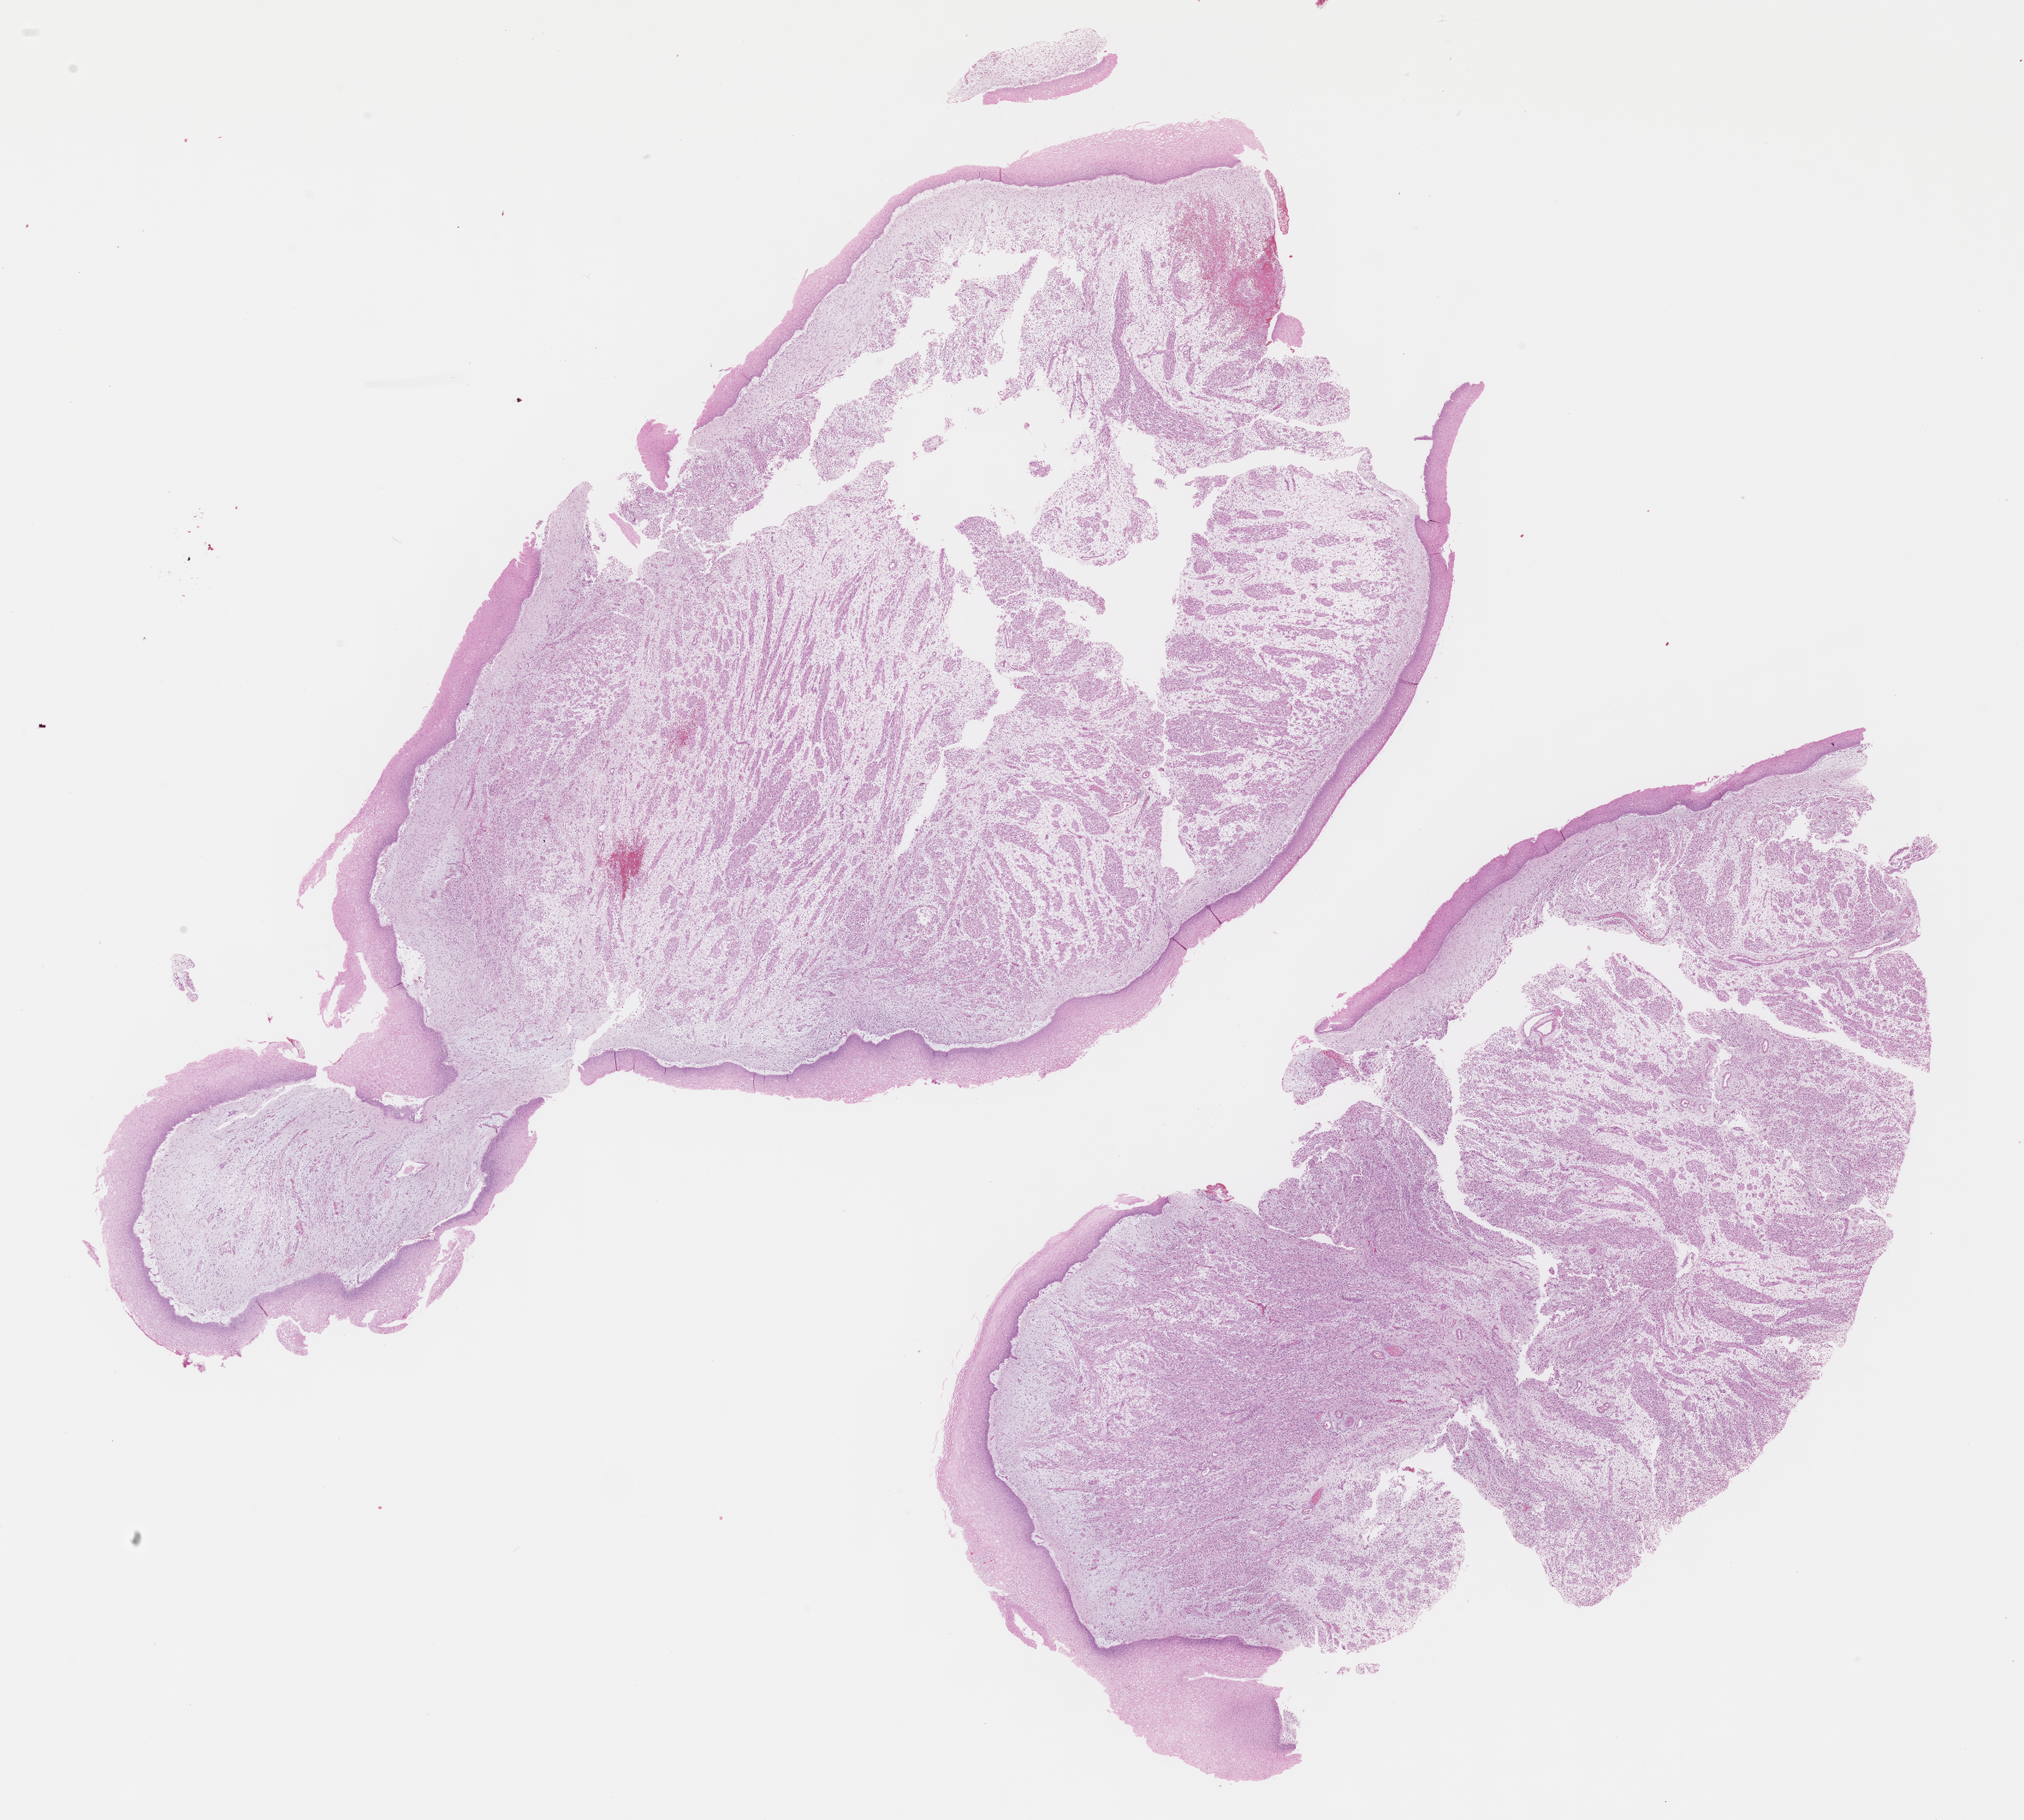
Hematoxylin and eosin (H&E) whole-slide image of tumor tissue, low-resolution overview of the scanned area, about 19.1 x 17.2 mm. Formalin-fixed paraffin-embedded section. Sample anatomic site: vagina. Female patient, age at diagnosis 2.1 years.
Diagnosis: rhabdomyosarcoma; histological classification: embryonal rhabdomyosarcoma. Stage (as recorded): 3.